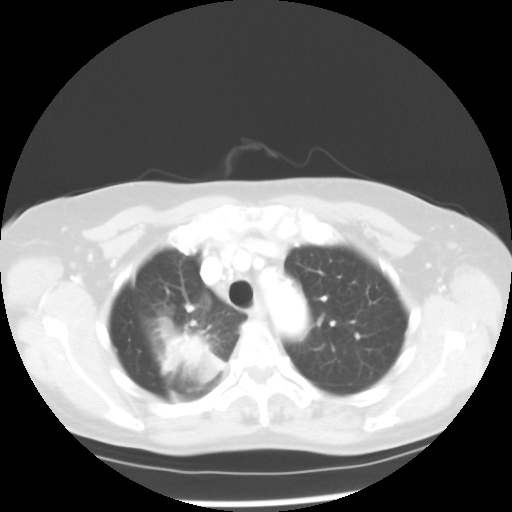
Chest CT, one axial slice; slice 40 of 52 in the series (ordered by position); reconstruction kernel STANDARD; 100 kVp; lung window (W 1500 / L -600 HU); 5 mm slice thickness; 512 × 512 image matrix. Patient: female, 60 years. Case-level facts recorded for this patient, not image findings: clinical TNM (as recorded): T2 N1 M1a.
Outlined on this slice (rectangle marked by the reading radiologist):
- lung tumour (recorded histology: adenocarcinoma): bounding box [x1, y1, x2, y2] px = [160, 330, 225, 387]